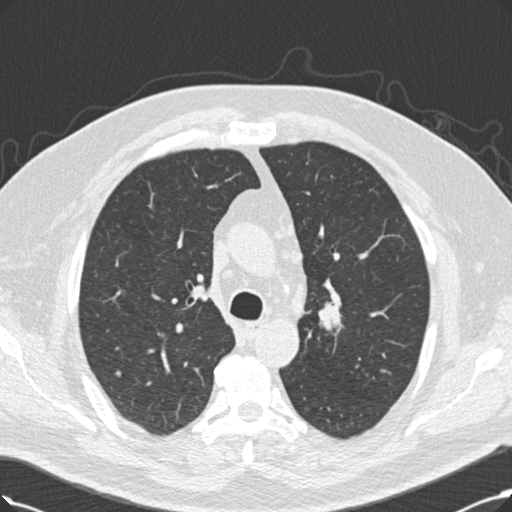
Low-dose screening chest CT, one axial slice; slice 154 of 214 in the series (ordered by position); reconstruction kernel B30f; 120 kVp; lung window (W 1500 / L -600 HU); 2 mm slice thickness; 512 × 512 image matrix, field of view 365 × 365 mm.
Annotated regions visible in this slice (outlined manually by an expert reader):
- lesion 1 (tumor): bounding box [x1, y1, x2, y2] px = [319, 303, 342, 335]